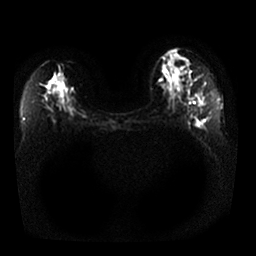
Breast MRI, one axial slice; diffusion-weighted series; image 2 of 4 stored at this slice position (different b-values; order by instance number); 1.5 T; 4 mm slice thickness; 256 × 256 image matrix. Female patient.
Annotated regions visible in this slice (outlined manually by an expert reader):
- tumour on diffusion-weighted imaging: bounding box <200,101,204,105> (left, top, right, bottom; pixels)